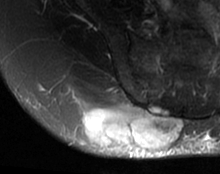
MRI of an extremity soft-tissue mass, one axial slice; slice 41 of 63 in the series (ordered by position); T2-weighted fat-saturated; MR volume resampled by the dataset authors to the PET/CT grid (not the native acquisition matrix); 220 × 174 image matrix, field of view 215 × 170 mm. Female patient. Case-level facts recorded for this patient, not image findings: histological type: spindle cell suggestive of myxofibrosarcoma; grade: intermediate; site of the primary tumour: right buttock.
Outlined on this slice (expert contour drawn on MRI and transferred to this co-registered scan by the dataset authors):
- gross tumour volume (mass): bounding box (x1, y1, x2, y2) in pixels: (81, 104, 183, 151)